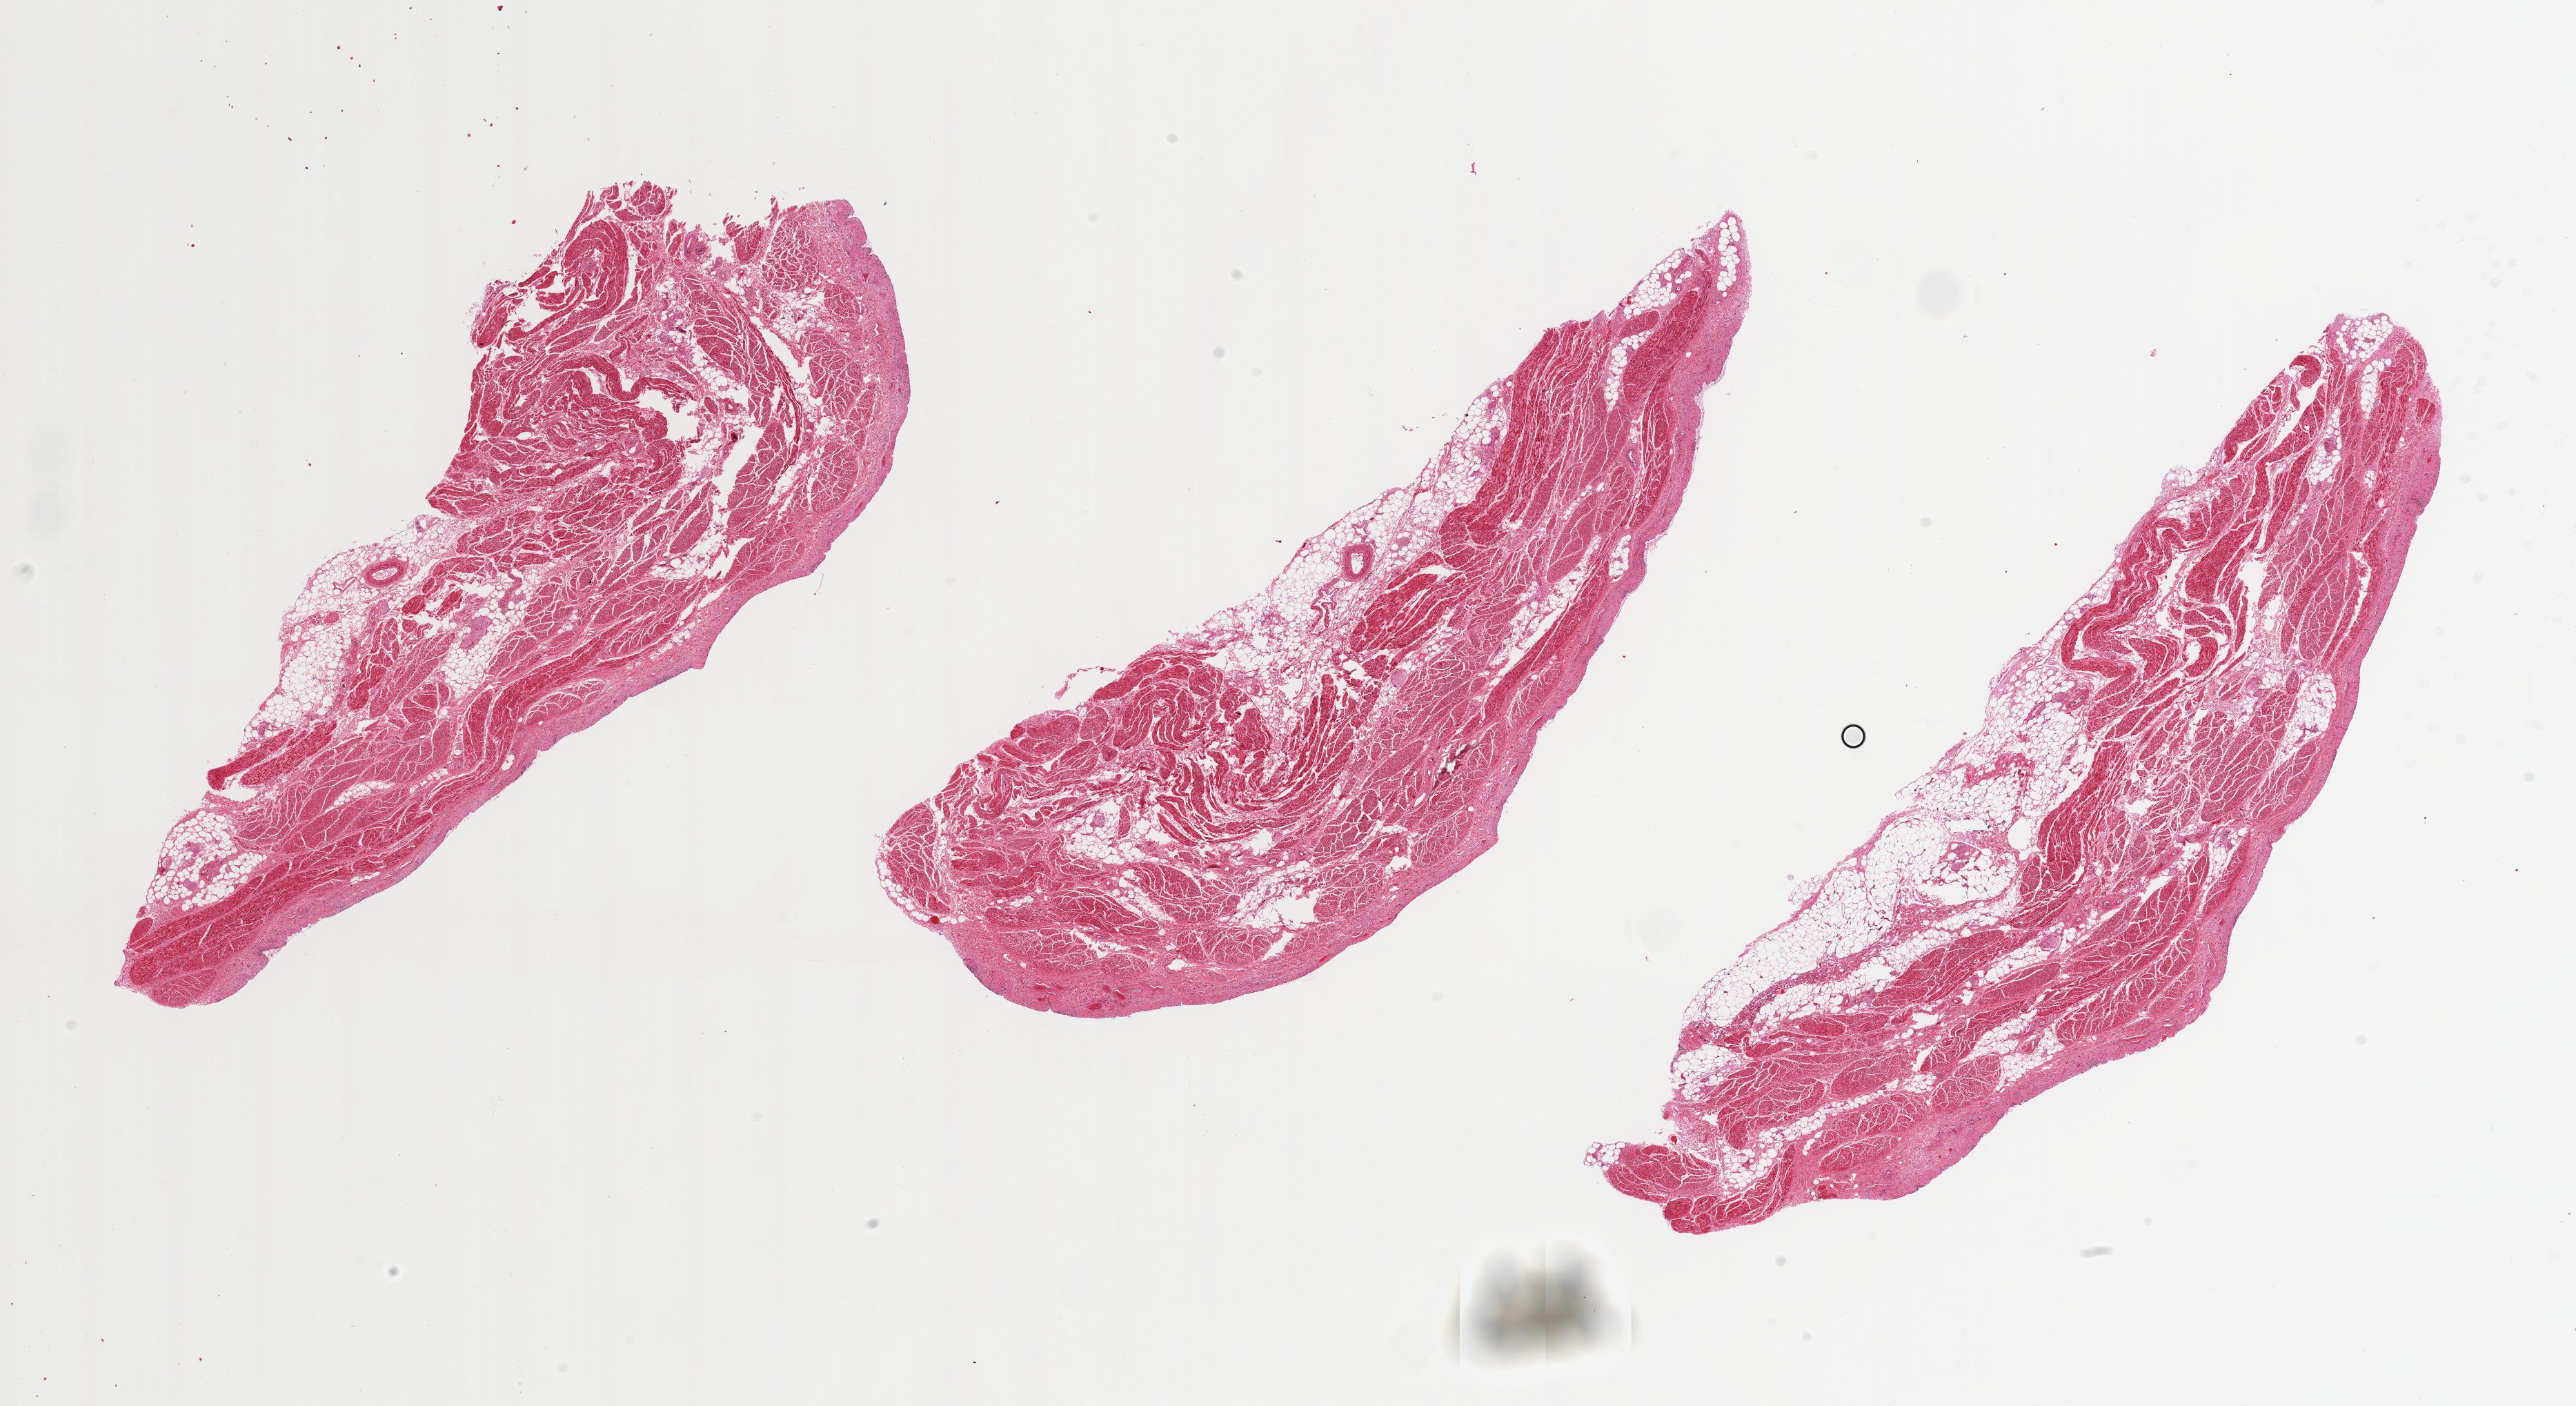
H&E whole-slide image, low-resolution overview of the scanned area, about 29.5 x 16.1 mm (acquisition: 20x scan). PAXgene-fixed, paraffin-embedded tissue. Sampled site (target tissue): urinary bladder. Donor tissue sample. Donor: male.
Pathologist's review note for this sample: Epithelium completely sloughed/autolyzed.